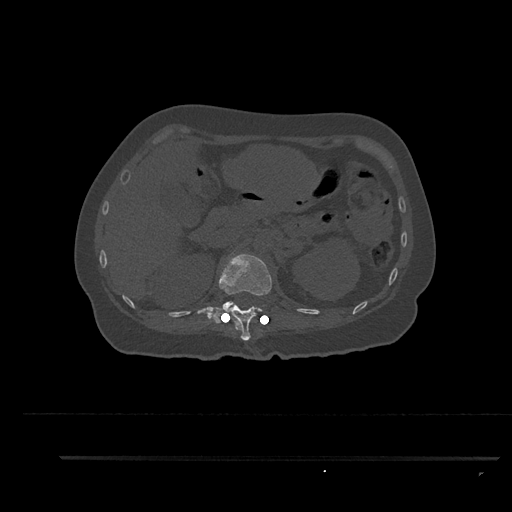
CT including the spine, one axial slice; slice 244 of 797 in the series (ordered by position); 120 kVp; bone window (W 1800 / L 400 HU); 512 × 512 image matrix. Female patient, age 44 years. From the clinical record (not read from this slice): primary cancer: renal.
Annotated regions visible in this slice (semi-automatic segmentation, software-assisted and operator-edited):
- L1 vertebra: bounding box <223,301,233,309> (left, top, right, bottom; pixels)
- T12 vertebra: <199,253,272,341>